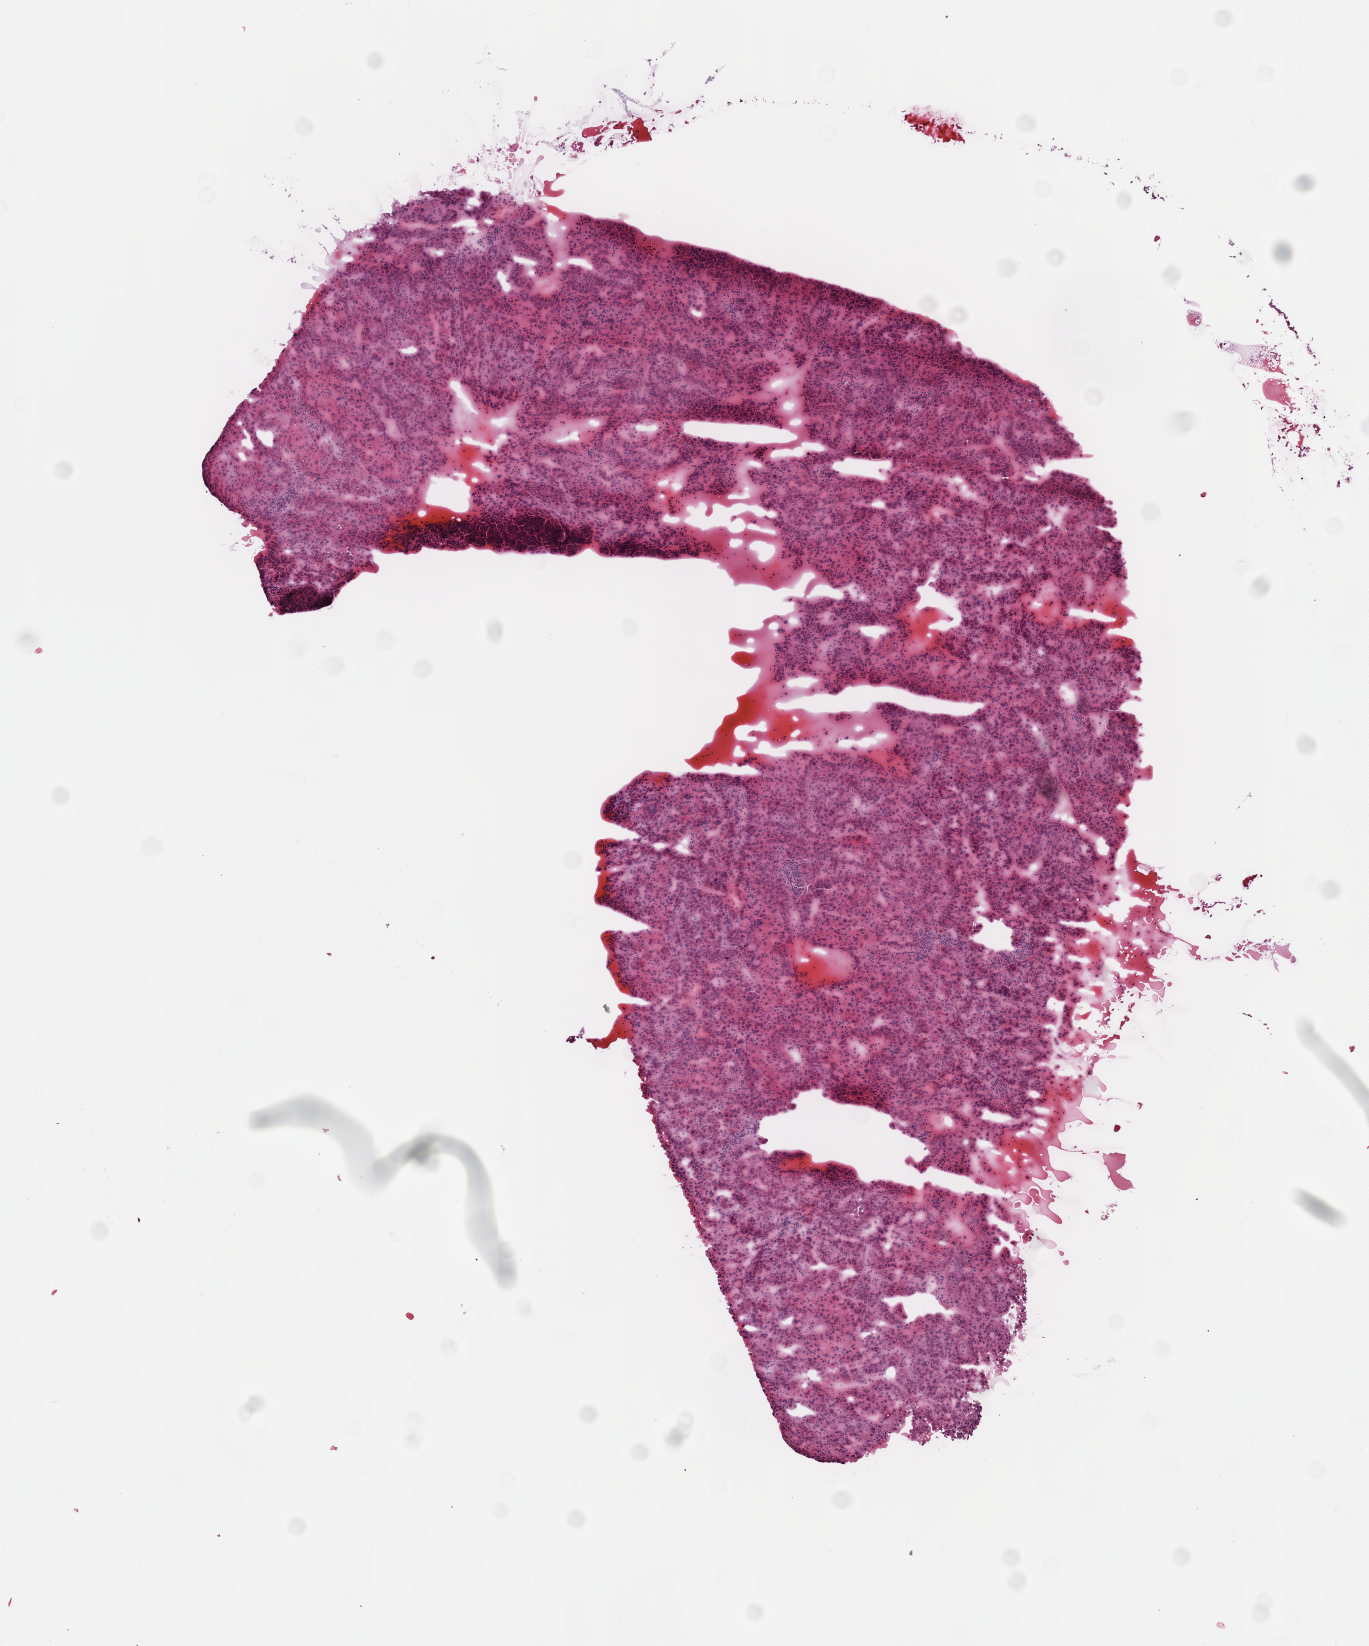
Hematoxylin and eosin (H&E) stained whole-slide image — low-resolution overview of the scanned area, about 5.5 x 6.7 mm (acquisition: 40x scan), frozen section from the top of the tissue portion, sample: primary tumour, liver. Male patient; age at initial diagnosis 55 years. Histologic grade: G3 (poorly differentiated). Composition of this section per pathologist review: tumour cells 85%, tumour nuclei 95%, normal cells 0%, stromal cells 10%, necrosis 5%. Inflammatory infiltration, as recorded: lymphocyte infiltration 0%, monocyte infiltration 0%, neutrophil infiltration 0%.
• TNM: T1 N0 M0
• AJCC pathologic stage: I (7th edition)
• diagnosis: Hepatocellular carcinoma, NOS